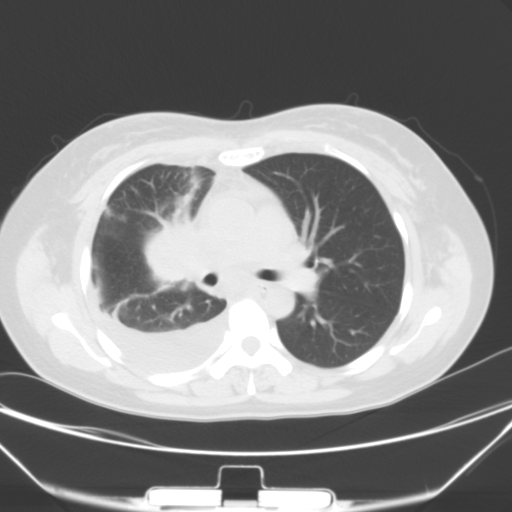
Chest CT, one axial slice. Slice 20 of 40 in the series (ordered by position). 120 kVp. Lung window (W 1500 / L -600 HU). 512 × 512 image matrix. Female patient, age 36 years. Case-level facts recorded for this patient, not image findings: clinical TNM (as recorded): T1b N2 M0.
Outlined on this slice (bounding box drawn by a radiologist):
- lung tumour (recorded histology: adenocarcinoma): bounding box (x1, y1, x2, y2) in pixels: (139, 215, 202, 287)